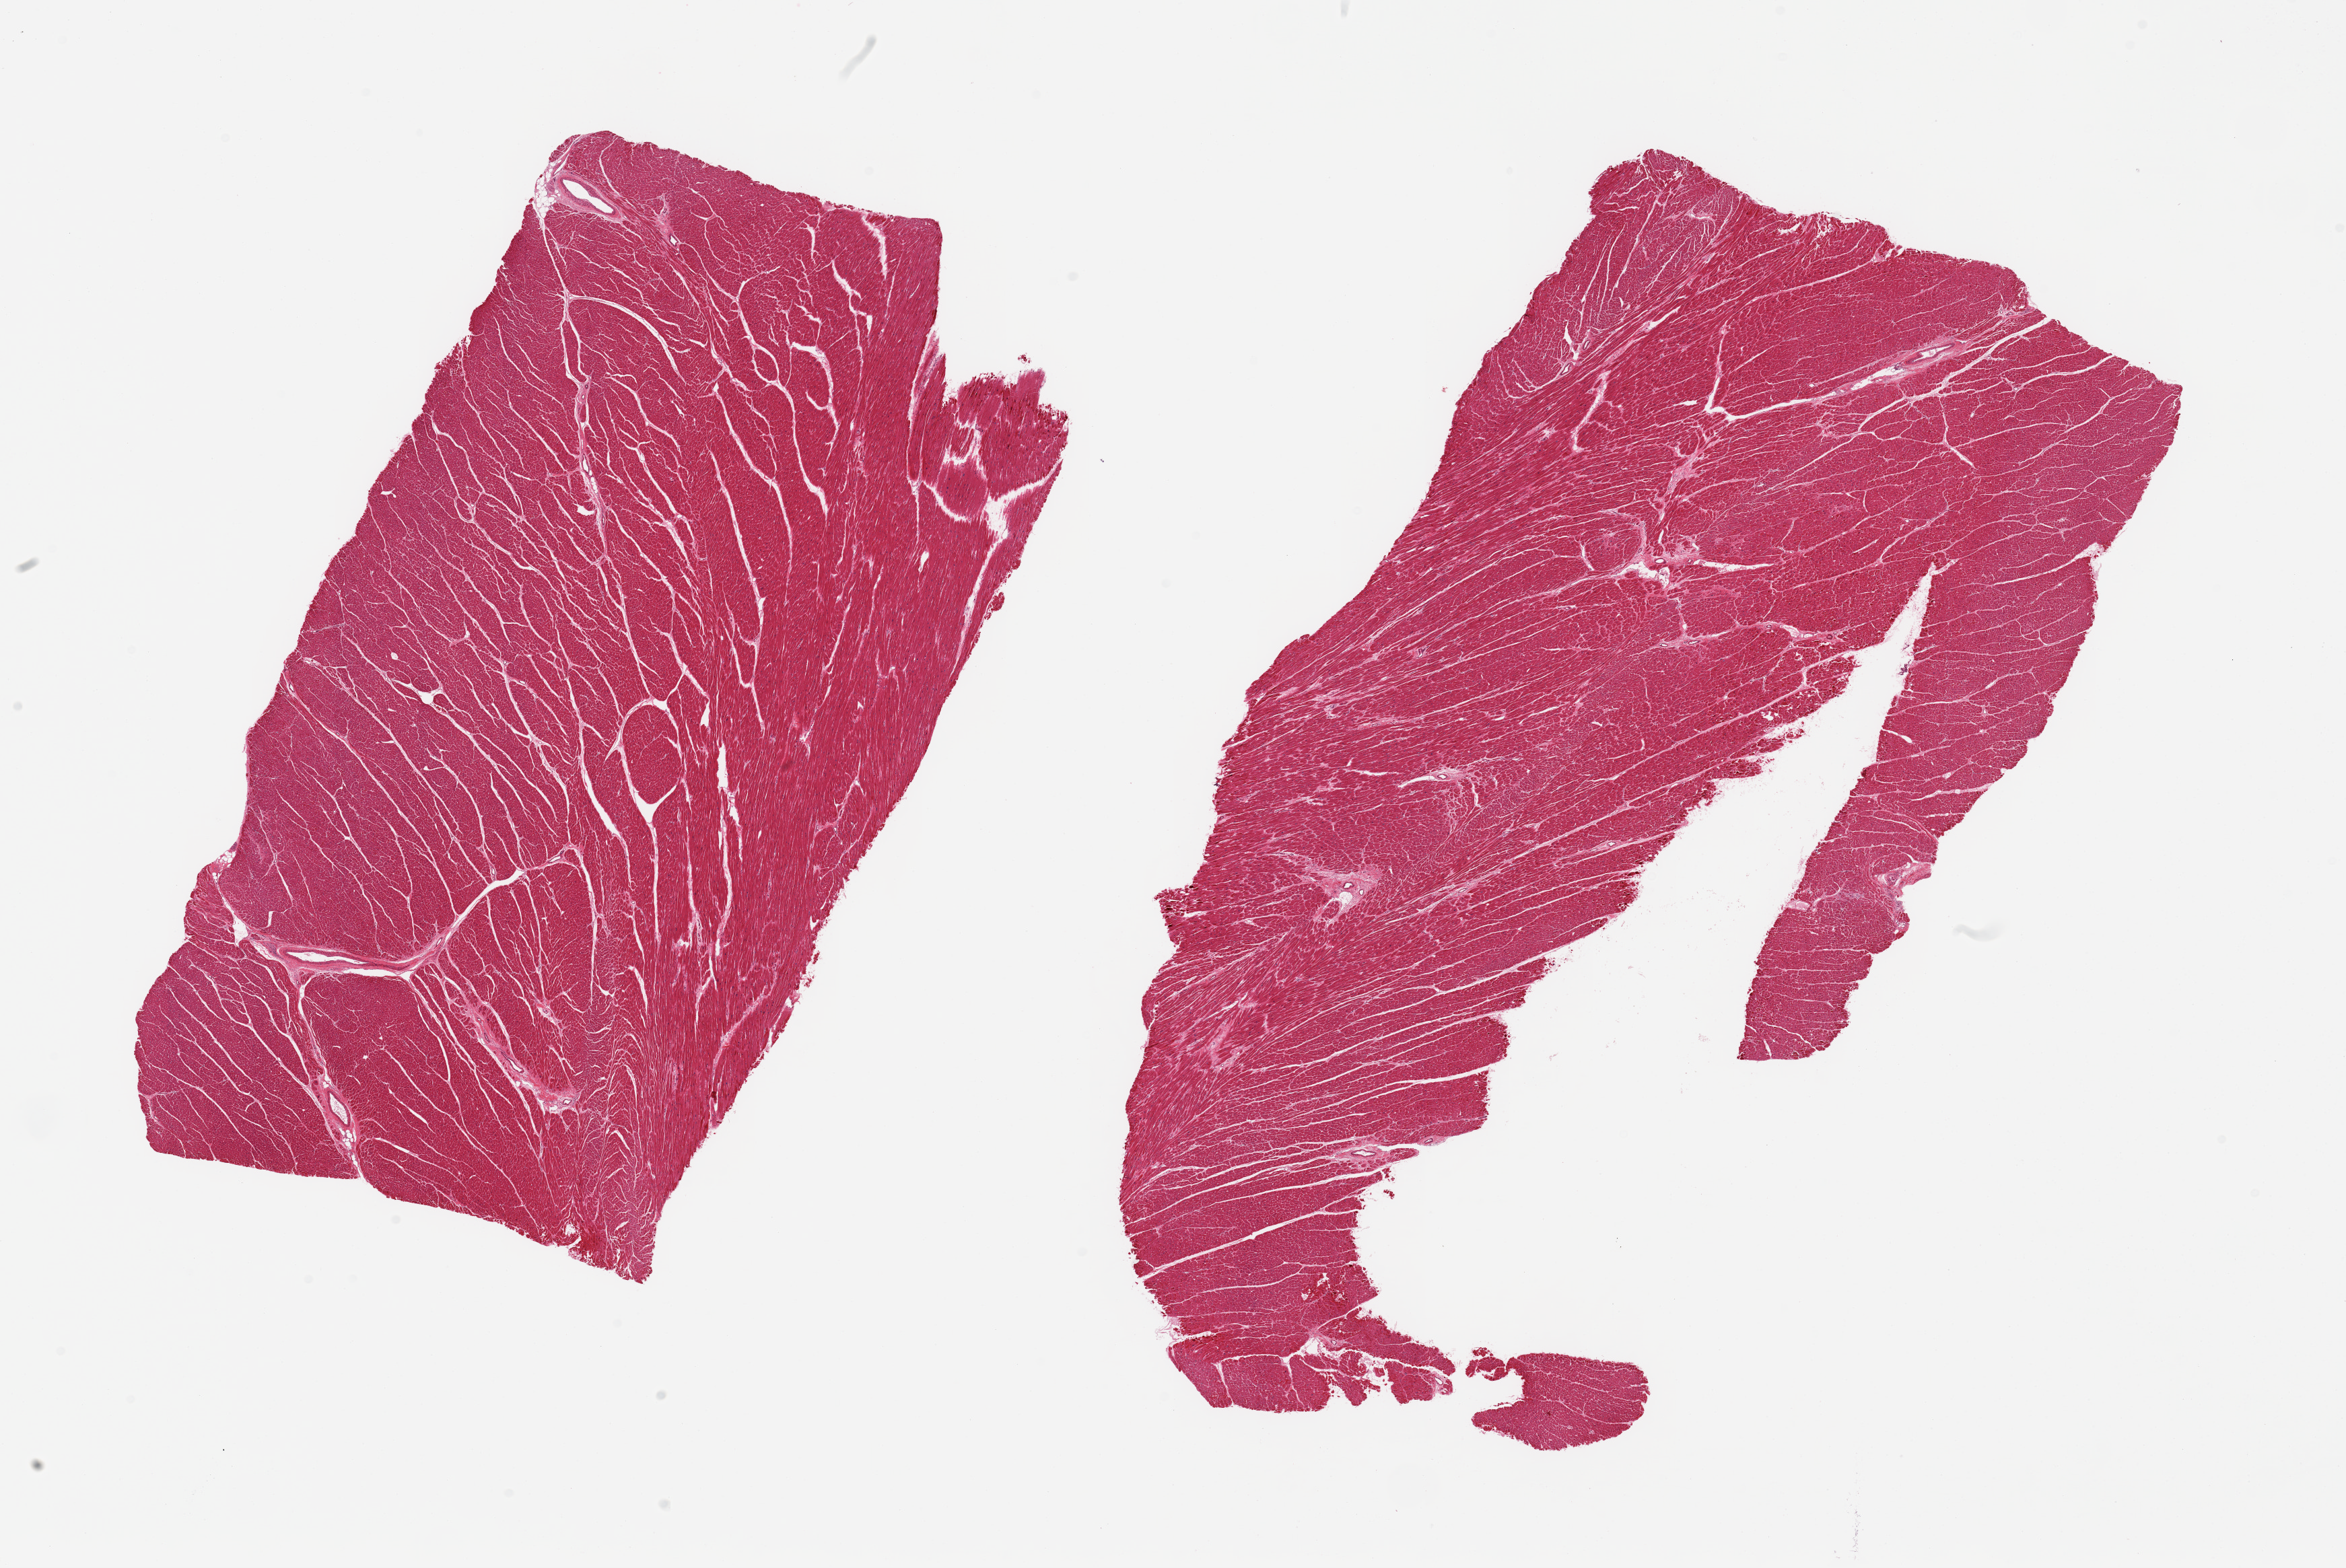
Digitized hematoxylin and eosin (H&E)-stained section — low-resolution overview of the scanned area, about 27.6 x 18.4 mm; PAXgene-fixed paraffin-embedded (PFPE) section; sampled site (target tissue): heart; tissue donor sample. Male donor.
- reviewer comment on this tissue sample: 2 pieces